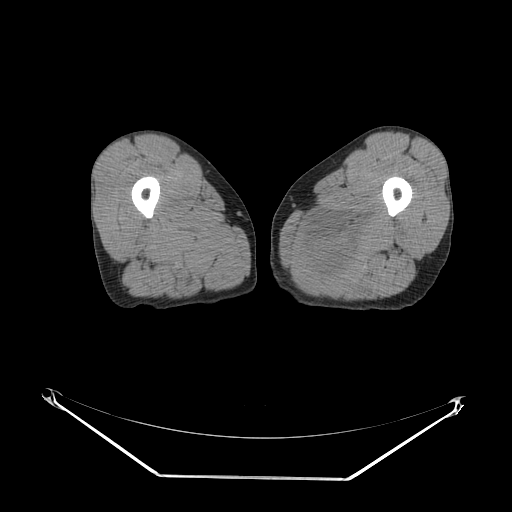
CT of an extremity soft-tissue mass (from a PET/CT study), one axial slice; slice 15 of 267 in the series (ordered by position); reconstruction kernel SOFT; soft-tissue window (W 400 / L 40 HU); 512 × 512 image matrix, field of view 500 × 500 mm. Male patient. From the clinical record (not read from this slice): histological type: pleiomorphic liposarcoma; grade: high; site of the primary tumour: left thigh.
Outlined on this slice (expert contour drawn on MRI and transferred to this co-registered scan by the dataset authors):
- gross tumour volume including surrounding oedema: box from (x=306, y=205) to (x=375, y=282) px
- gross tumour volume (mass): (x=313, y=242)–(x=359, y=277)